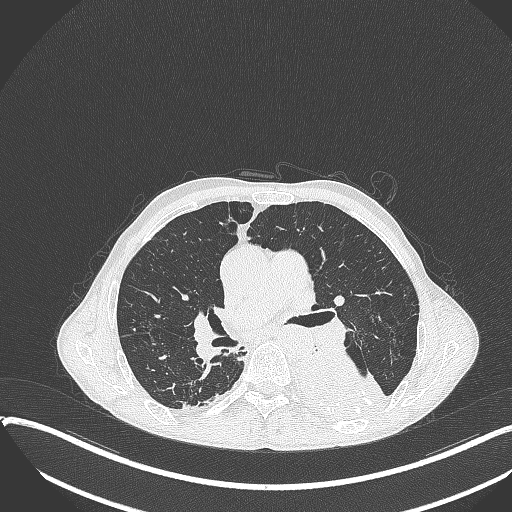
Chest CT, one axial slice. Slice 218 of 401 in the series (ordered by position). Reconstruction kernel B70f. 120 kVp. Lung window (W 1500 / L -600 HU). 1 mm slice thickness. 512 × 512 image matrix, field of view 400 × 400 mm. Patient: male, 57 years. From the clinical record (not read from this slice): clinical TNM (as recorded): T4 N0 M0.
Structures marked on this image (bounding box drawn by a radiologist):
- lung tumour (recorded histology: squamous cell carcinoma): bounding box (x1, y1, x2, y2) in pixels: (290, 353, 390, 423)